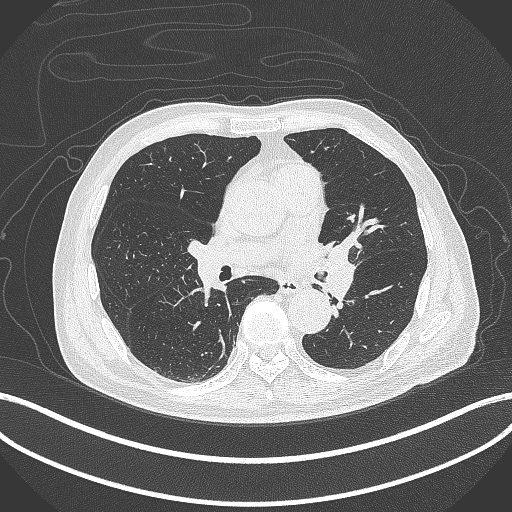
Chest CT, one axial slice. Position 227 of 417 along the scan axis. Reconstruction kernel B70f. Lung window (W 1500 / L -600 HU). 1 mm slice thickness. 512 × 512 image matrix, field of view 400 × 400 mm. Patient: male, 77 years. From the clinical record (not read from this slice): clinical TNM (as recorded): T3 N1 M0.
Outlined on this slice (bounding box drawn by a radiologist):
- lung tumour (recorded histology: adenocarcinoma): bounding box [x1, y1, x2, y2] px = [317, 238, 361, 308]